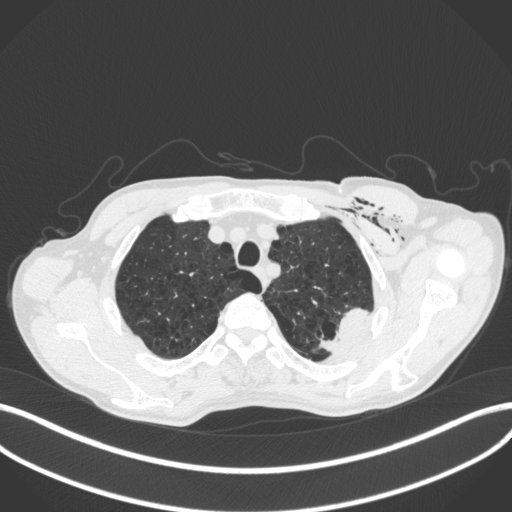
Chest CT, one axial slice. Slice 349 of 416 in the series (ordered by position). Lung window (W 1500 / L -600 HU). 1 mm slice thickness. 512 × 512 image matrix. Patient: male, 58 years. From the clinical record (not read from this slice): clinical TNM (as recorded): T3 N0 M0.
Structures marked on this image (rectangle marked by the reading radiologist):
- lung tumour (recorded histology: adenocarcinoma): bounding box [x1, y1, x2, y2] px = [318, 306, 368, 356]